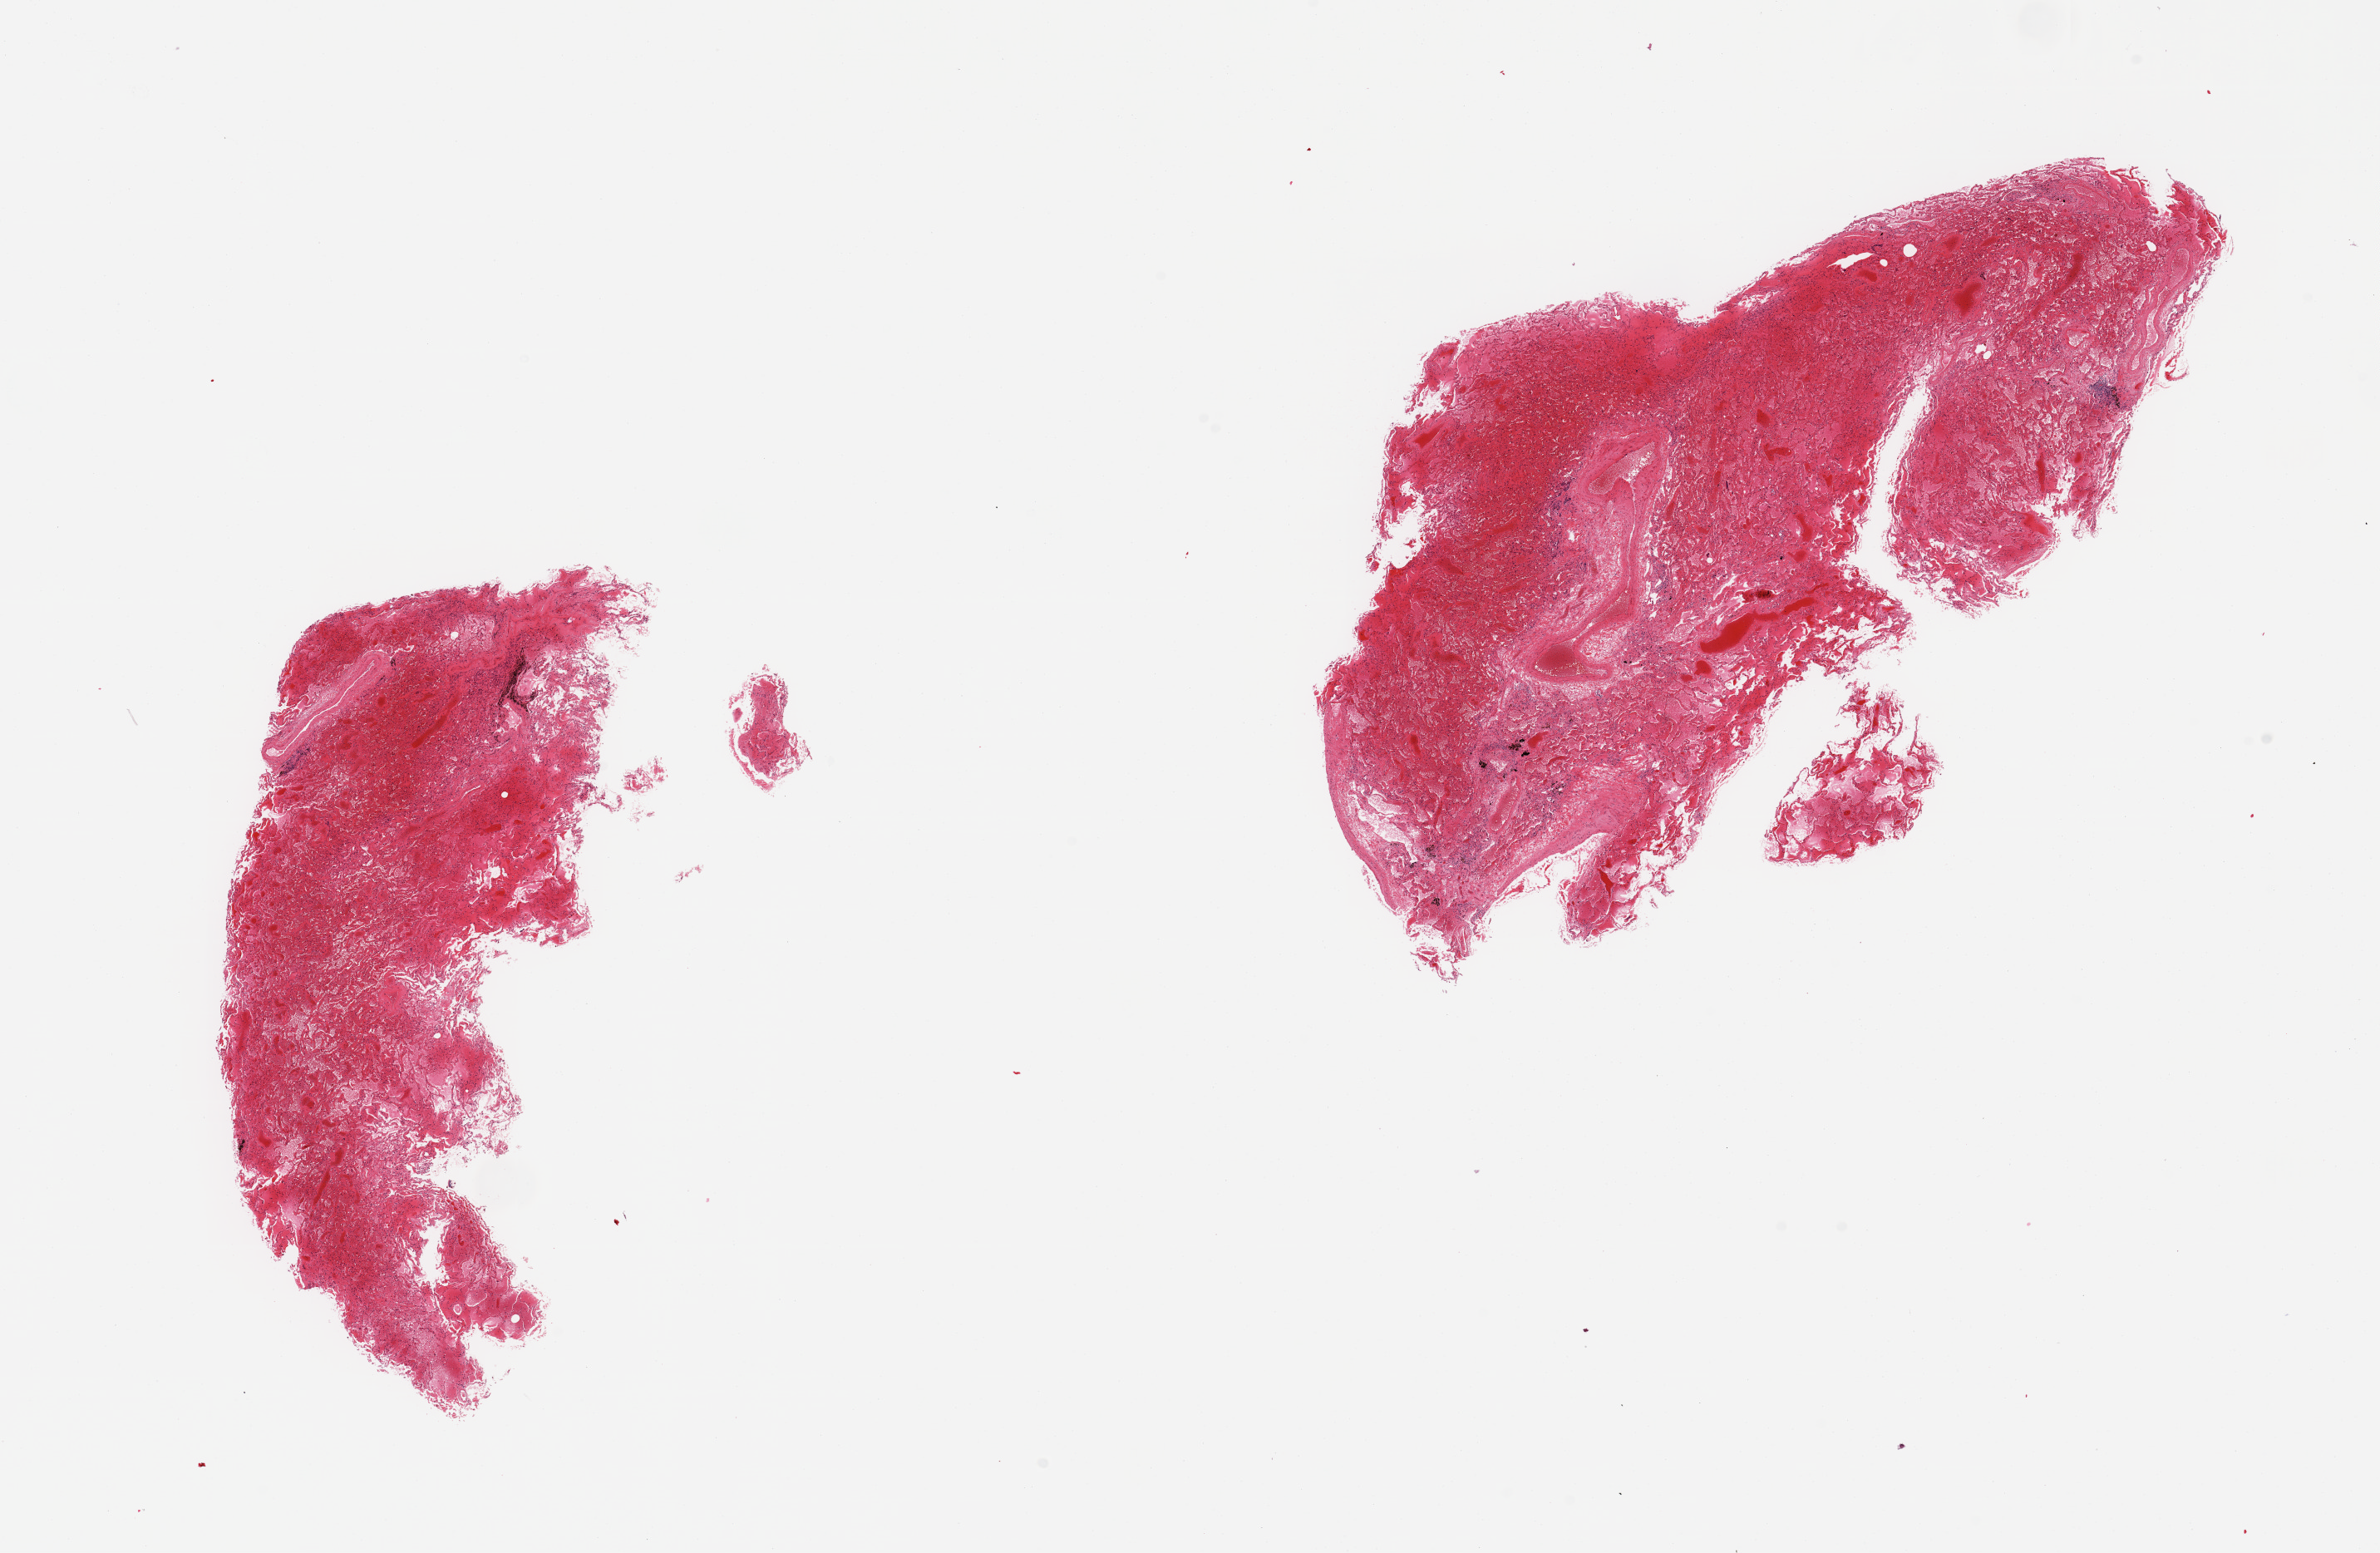
H&E whole-slide image, brightfield, low-resolution overview of the scanned area, about 22.6 x 14.8 mm (from a 20x scan), PAXgene-fixed, paraffin-embedded tissue, target tissue: lung, tissue donor sample. Donor sex: female.
- review note (as recorded): 2 pieces; extensive alveolar edema & hemorrhage